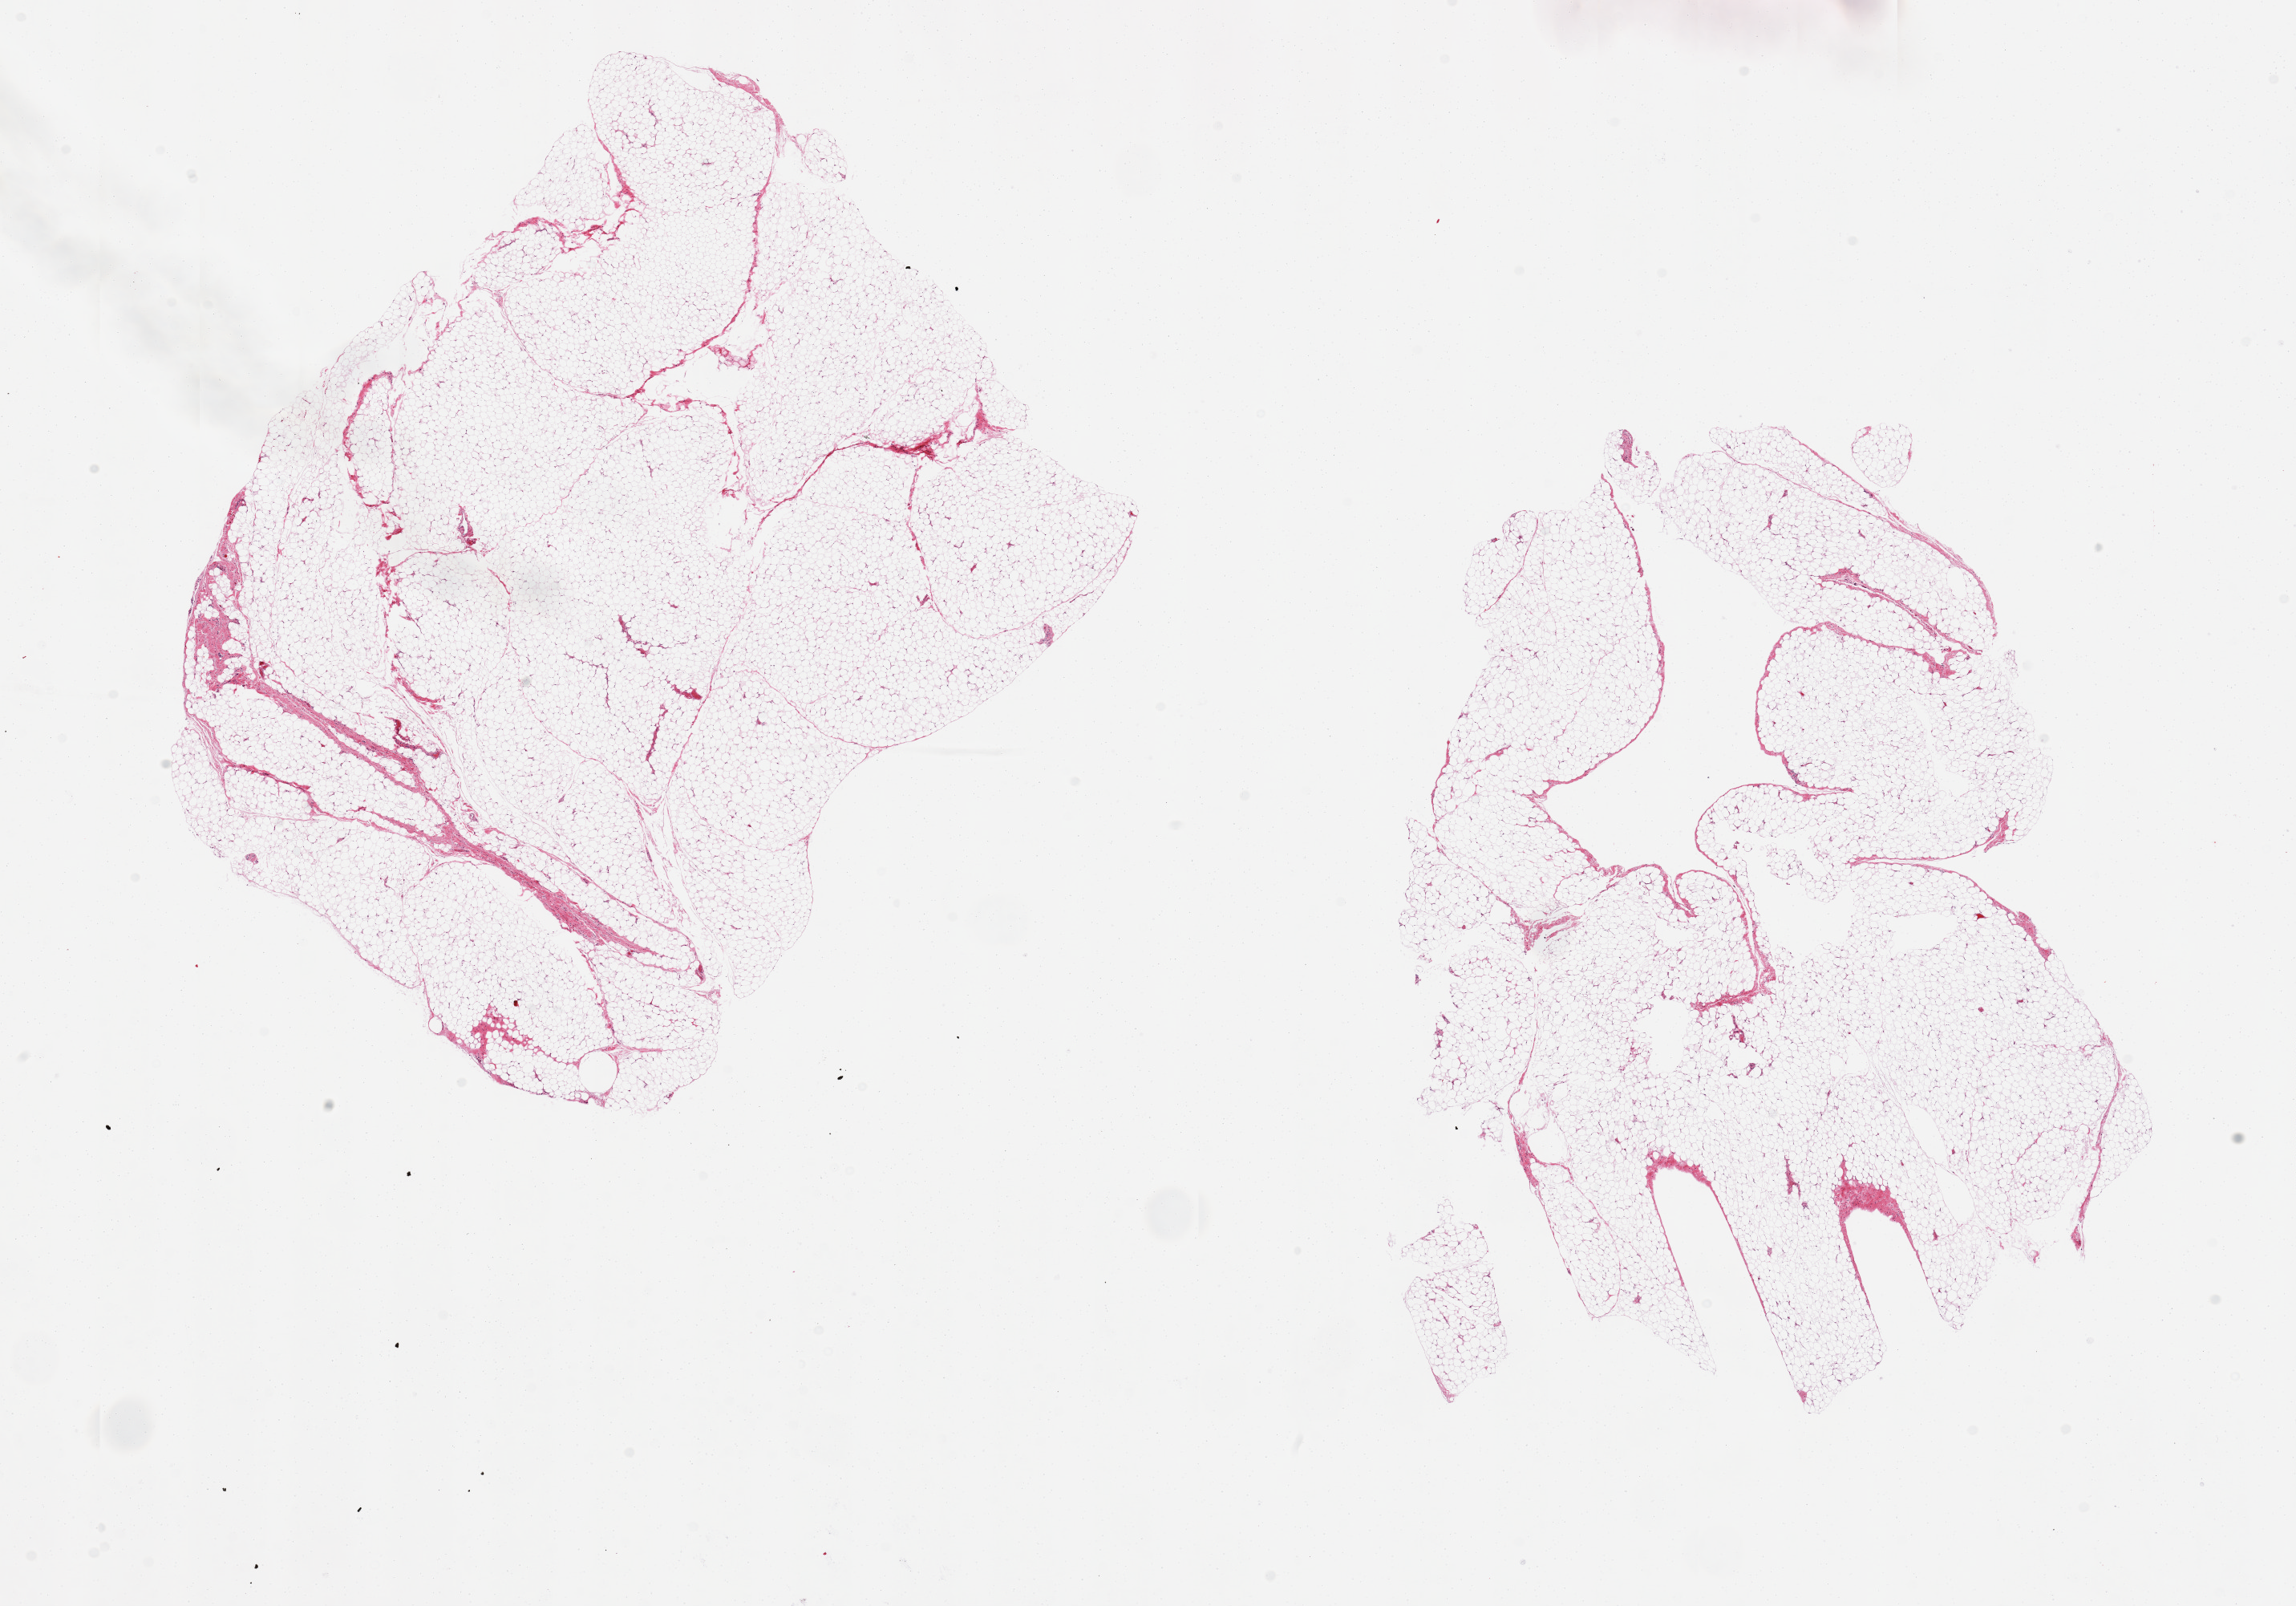
Whole-slide image, H&E stain, low-resolution overview of the scanned area, about 22.6 x 15.8 mm. PAXgene-fixed paraffin-embedded (PFPE) section. Target tissue: omentum. Donor tissue sample. Donor: male.
Reviewer comment on this tissue sample: 2 pieces.